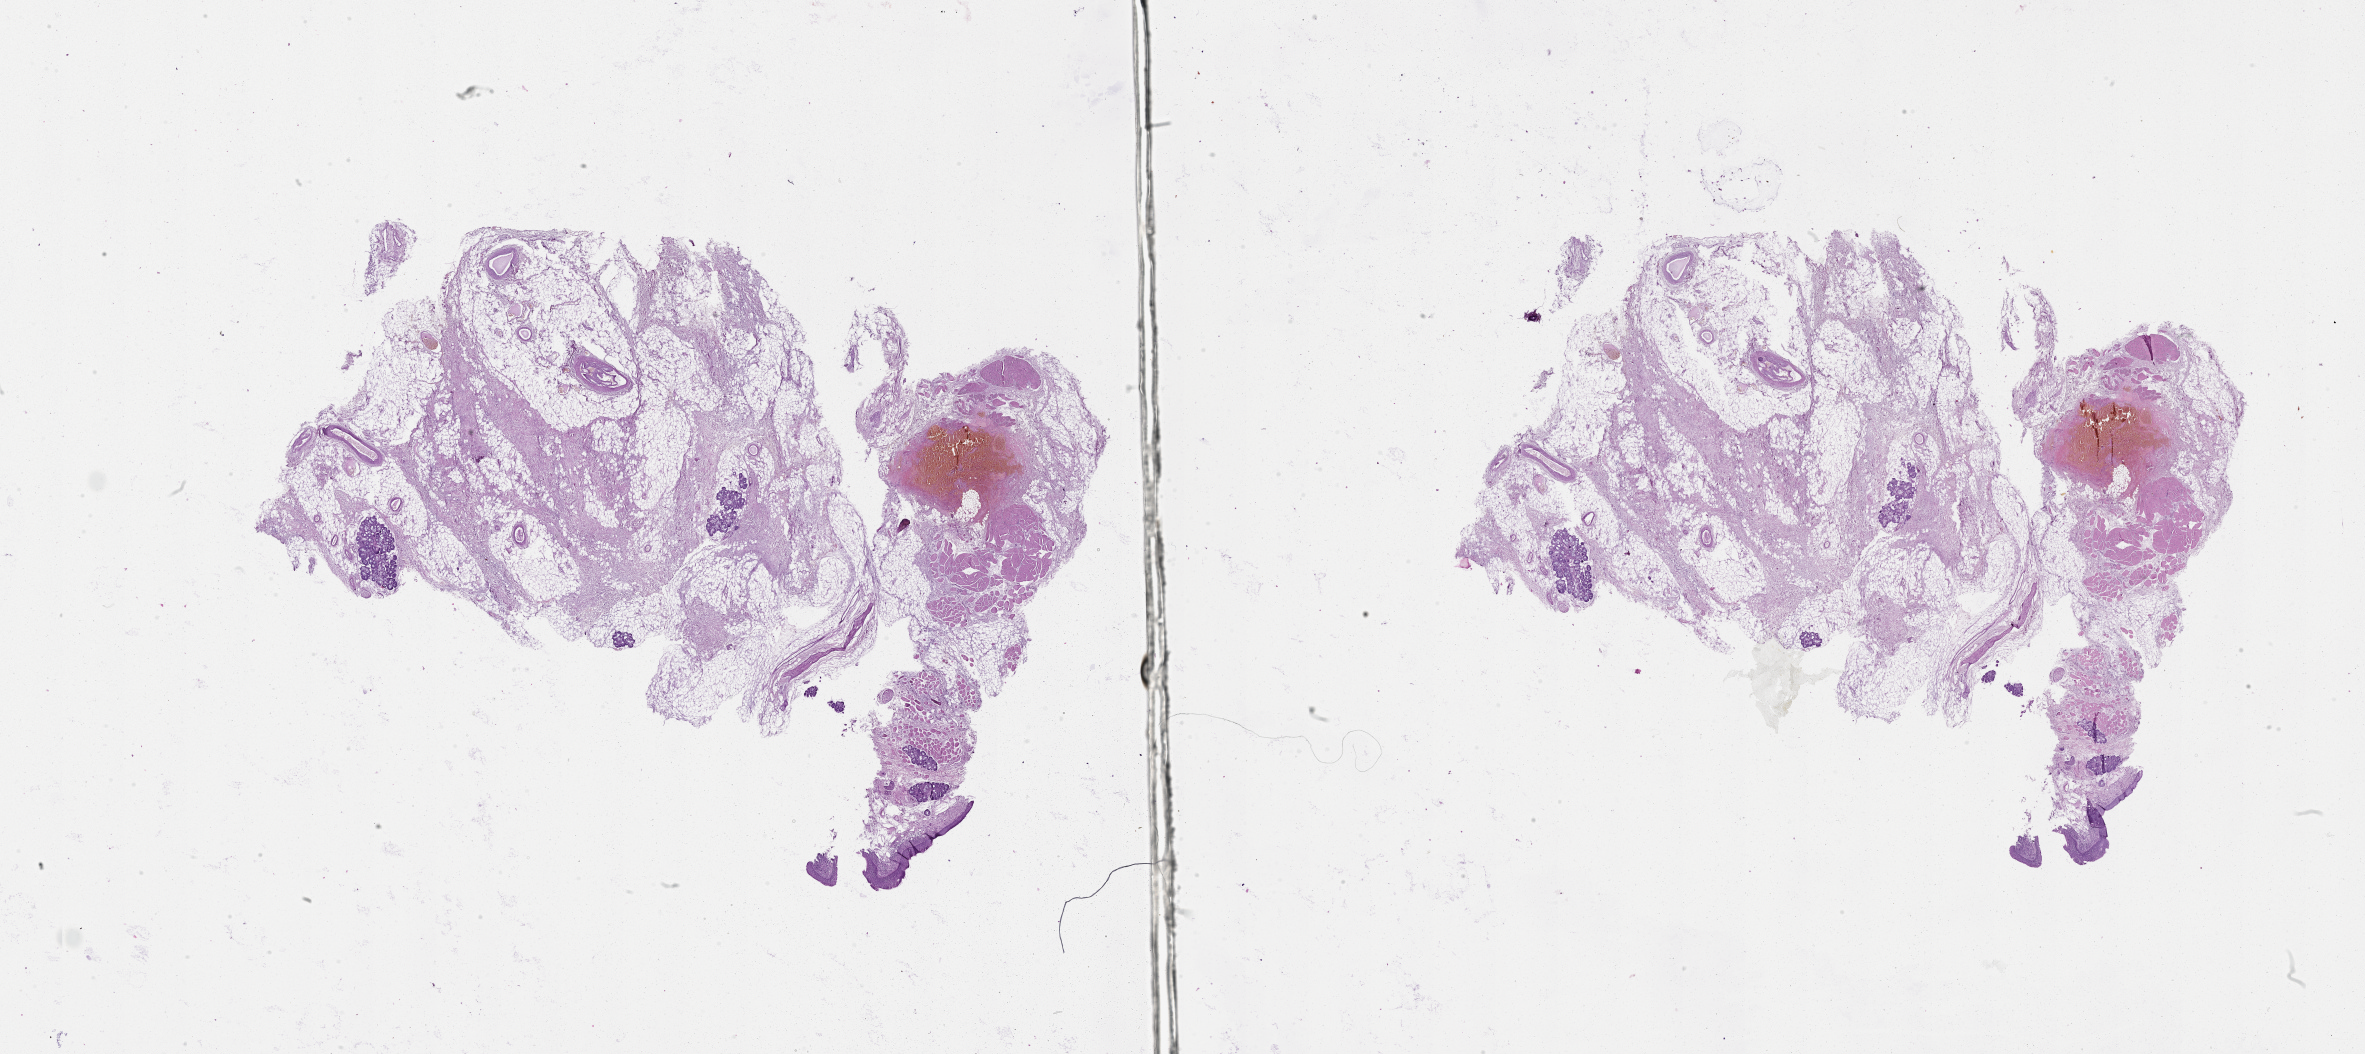
Whole-slide histology image, Hematoxylin and eosin (H&E) stained, whole scanned area (about 38.1 x 17.0 mm, acquisition: 20x scan) shown as a low-resolution overview. Normal (non-tumour) tissue sample, sampled site: larynx. 55-year-old male patient.
• this section: normal (non-tumour) tissue from the same patient
• patient diagnosis: Squamous cell carcinoma, NOS (larynx, NOS)